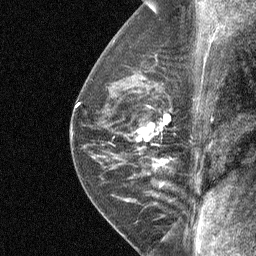
Breast MRI (dynamic contrast-enhanced), one sagittal slice. Slice 40 of 64 in the series (ordered by position). Dynamic contrast-enhanced study with each time point stored as its own series, time point 2 of 4 at this slice position (early post-contrast, ordered by acquisition time). 1.5 T. TE 4.8 ms, TR 27 ms. 256 × 256 image matrix, field of view 180 × 180 mm. Patient: female, 50 years. Case-level facts recorded for this patient, not image findings: setting: breast cancer imaged before/during neoadjuvant chemotherapy; receptor status: HER2-positive.
Structures marked on this image (semi-automatically segmented with operator editing):
- analysis volume of interest (the breast-tissue region the enhancement analysis was run in; not a lesion): box from (x=123, y=91) to (x=177, y=177) px
- tumour enhancement mask (voxels above the 90 % enhancement threshold inside the analysis volume of interest): (x=137, y=115)–(x=170, y=161)